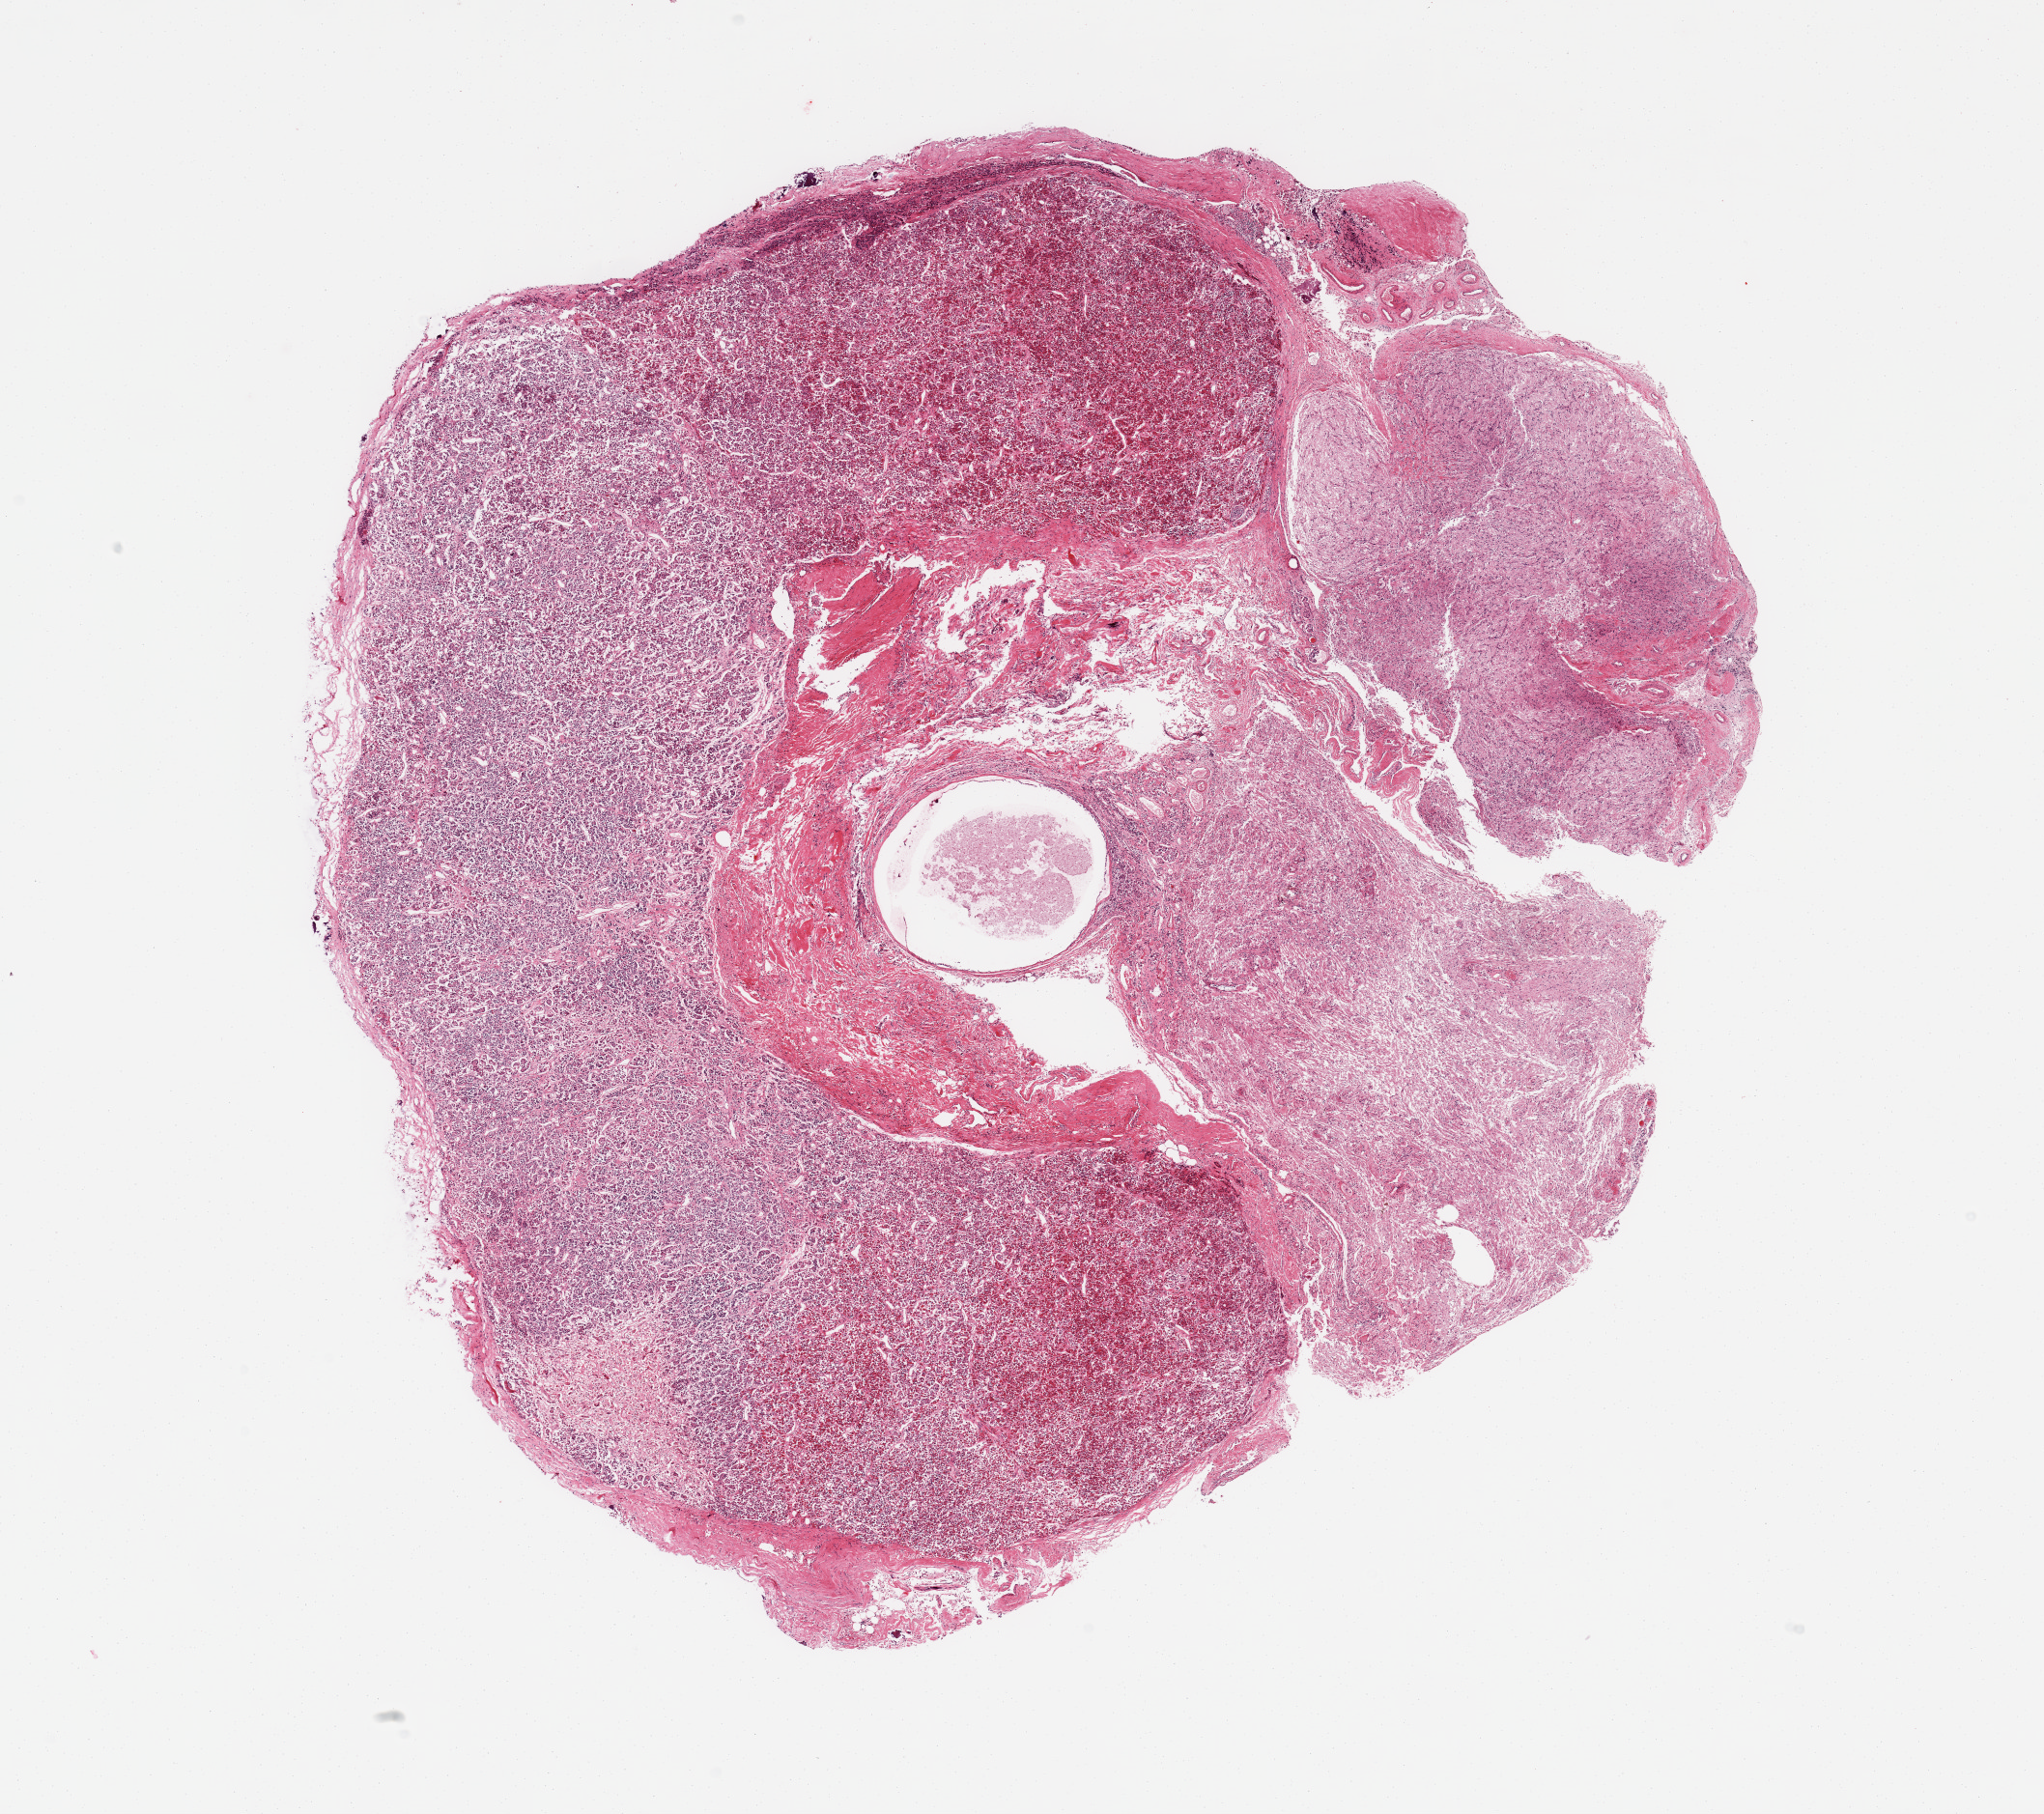
Whole-slide image, haematoxylin and eosin stain, low-resolution overview of the scanned area, about 16.7 x 14.9 mm (acquisition: 20x scan); PAXgene-fixed paraffin-embedded (PFPE) section; target tissue: pituitary; donor tissue sample.
• pathologist's review note for this sample: 1 piece; grade 1 and focally grade 2 autolyzed adenohypophysis and neurohypophysis; small 1.8mm in diameter cyst surrounded by fibrous tissue